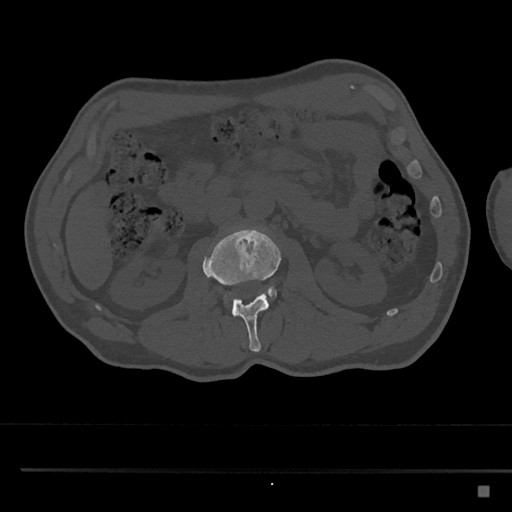
CT including the spine, one axial slice; slice 744 of 797 in the series (ordered by position); reconstruction kernel Br40s/3; 120 kVp; bone window (W 1800 / L 400 HU); 0.5 mm slice thickness; 512 × 512 image matrix, field of view 391 × 391 mm. Patient: male, 59 years. From the clinical record (not read from this slice): primary cancer: prostate.
Structures marked on this image (semi-automatic segmentation, software-assisted and operator-edited):
- L2 vertebra: bounding box (x1, y1, x2, y2) in pixels: (202, 227, 282, 352)
- L3 vertebra: (224, 286, 277, 305)